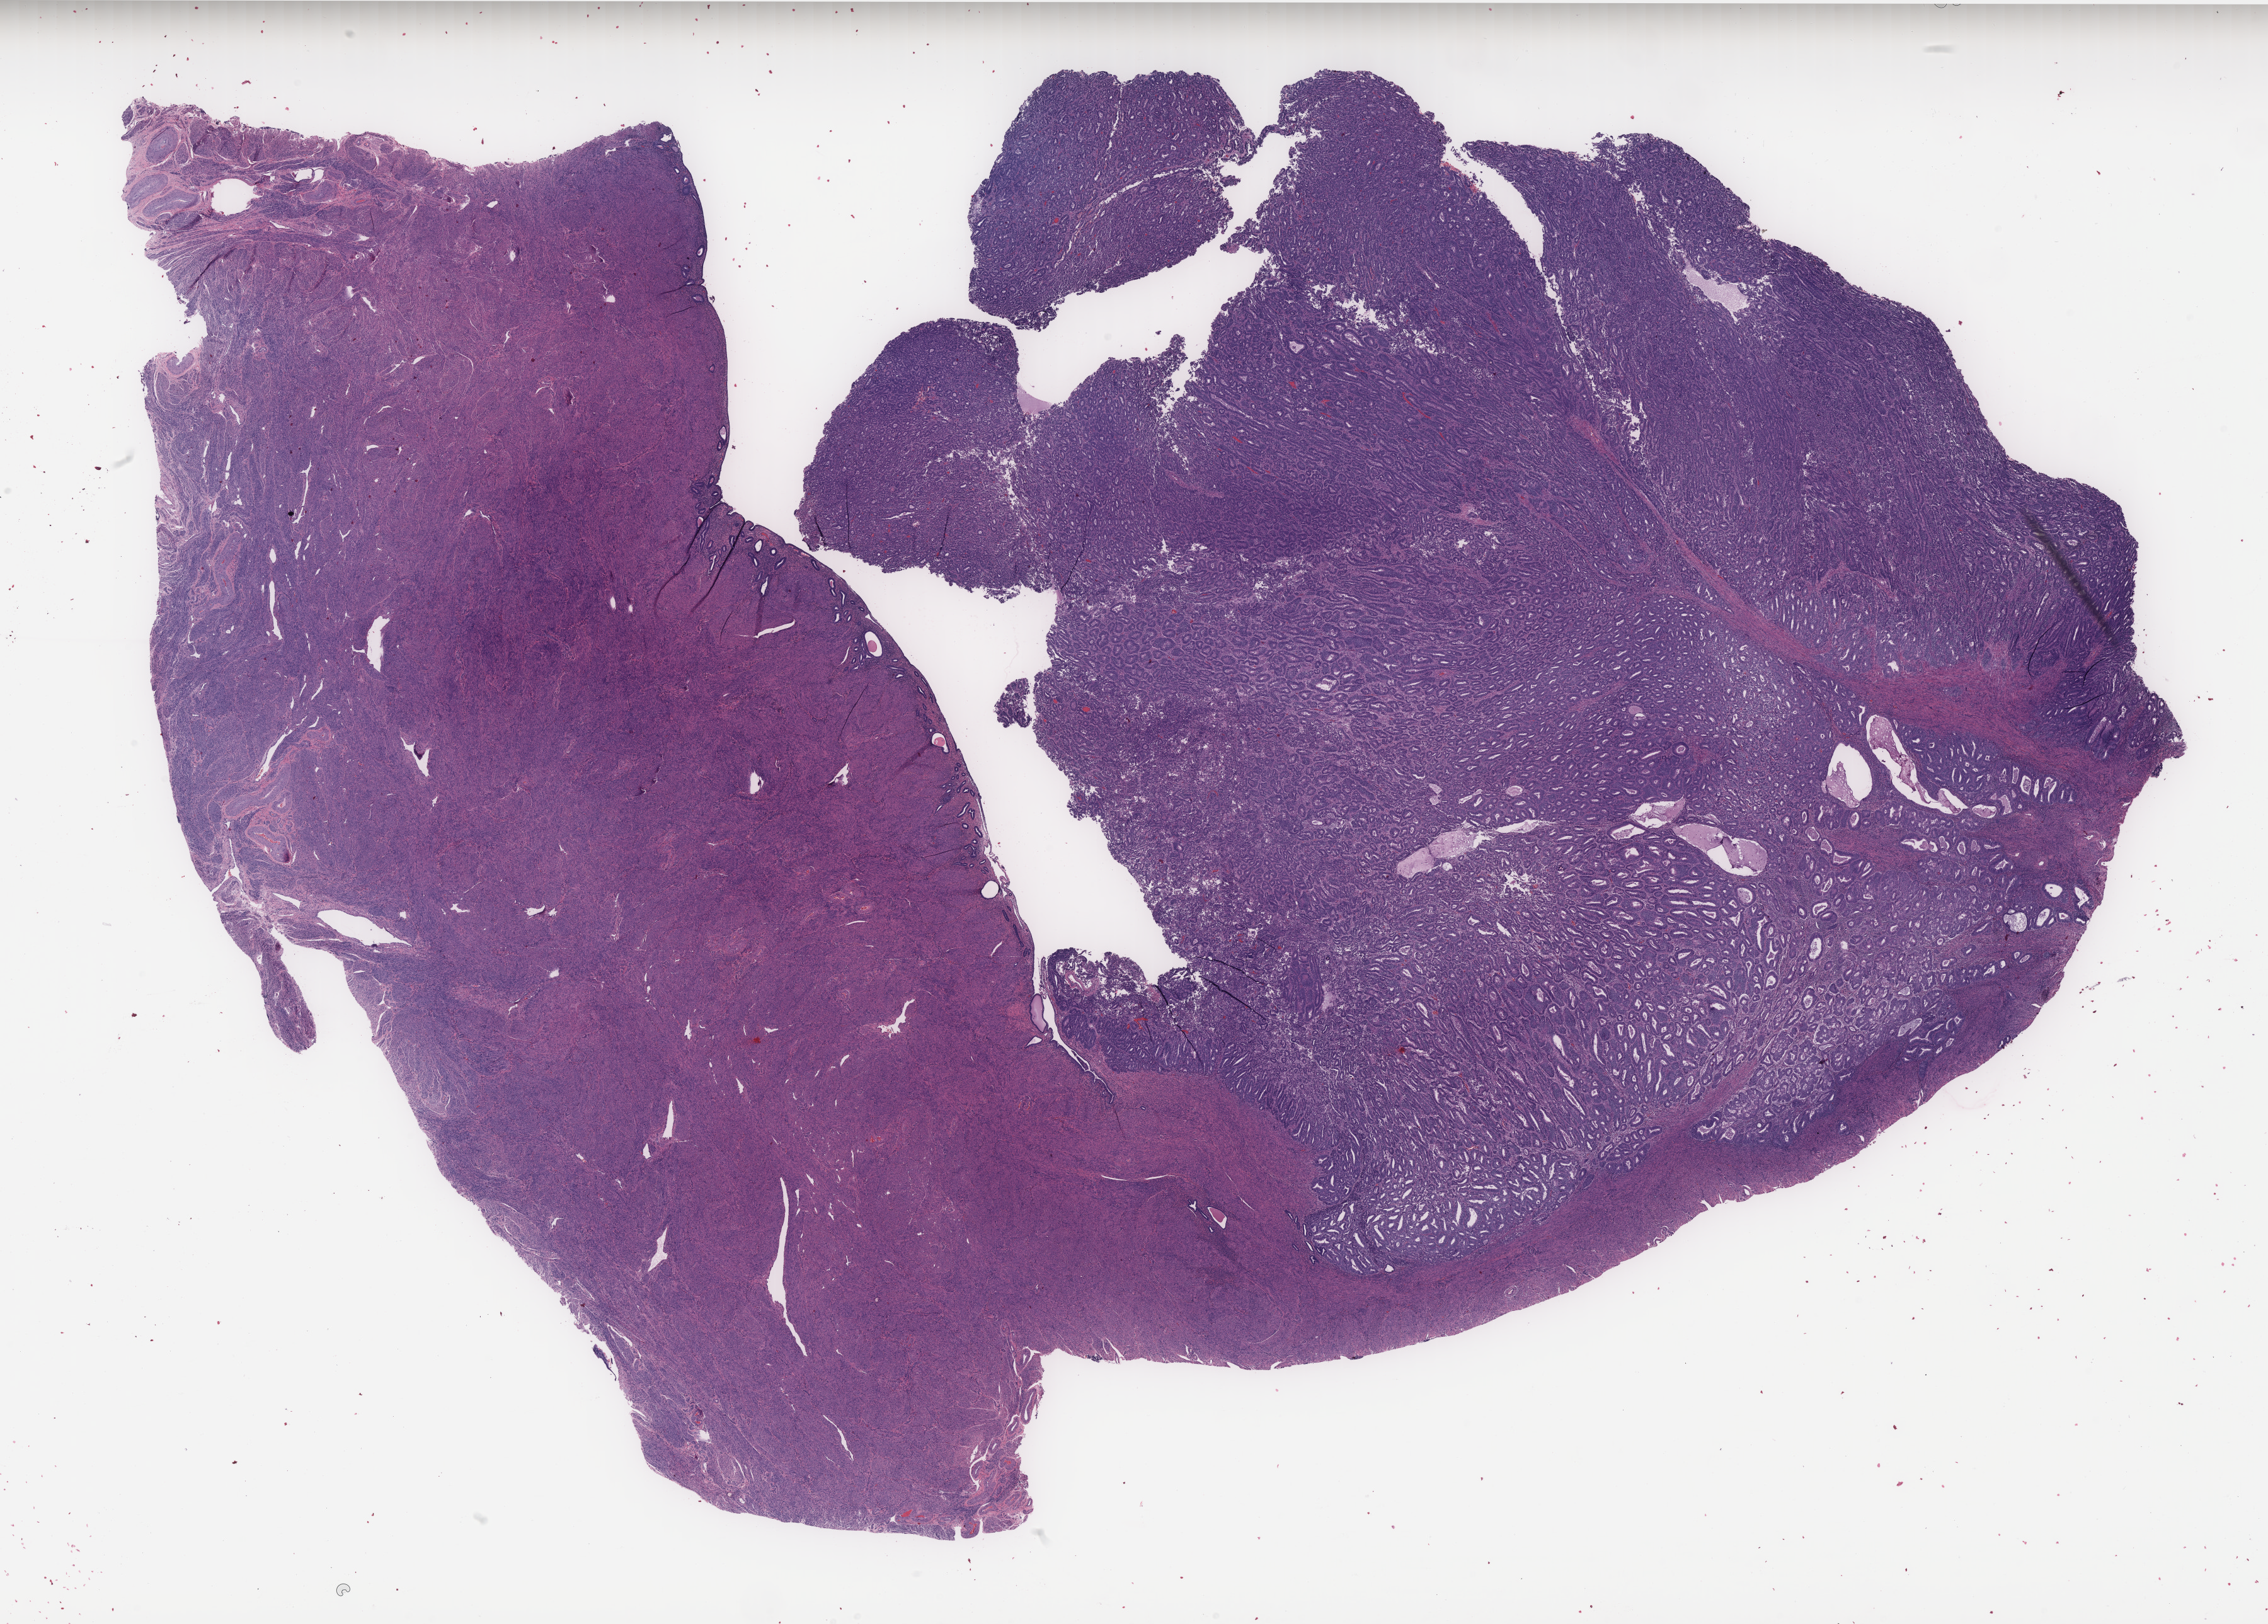
Whole-slide histology image, H&E — shown as a low-resolution overview of the whole scanned area (about 28.9 x 20.7 mm), formalin-fixed paraffin-embedded (FFPE) diagnostic section, uterus, primary tumour sample. Patient: female, age at initial diagnosis 64 years. Histologic grade: G2 (moderately differentiated).
Histologic diagnosis: Endometrioid adenocarcinoma, NOS (endometrium). FIGO stage: IA.